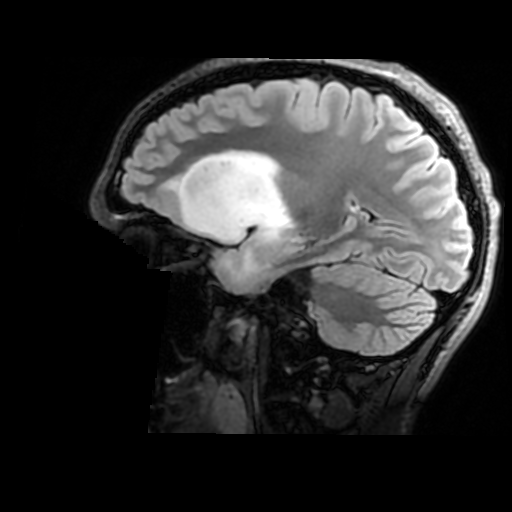
Brain MRI from a brain-tumour surgery series, one sagittal slice; slice 110 of 176 in the series (ordered by position); T2 FLAIR; 1 mm slice thickness; 512 × 512 image matrix, field of view 240 × 240 mm. From the clinical record (not read from this slice): histopathology: Astrocytoma; WHO grade: 2; IDH mutation: yes; tumour location: Right Insular.
Outlined on this slice (manually delineated by an expert):
- tumour: box from (x=175, y=151) to (x=291, y=286) px